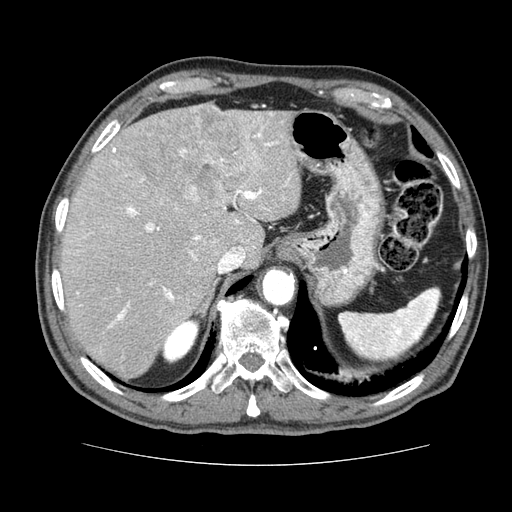
Contrast-enhanced abdominal CT (liver protocol), one axial slice; position 54 of 79 along the scan axis; soft-tissue window (W 400 / L 40 HU); 512 × 512 image matrix, field of view 360 × 360 mm. Case-level facts recorded for this patient, not image findings: diagnosis: hepatocellular carcinoma (patient treated with transarterial chemoembolisation; whether this scan precedes or follows treatment is not stated here); TNM stage (as recorded): Stage-I; Child-Pugh class: A; tumour nodularity: uninodular.
Outlined on this slice (semi-automatically segmented with operator editing):
- liver parenchyma outside the tumour (the mass and vessels are separate outlines, so this box may not span the whole liver): bounding box [x1, y1, x2, y2] px = [60, 102, 300, 378]
- mass: [141, 103, 250, 202]
- liver vessels: [76, 112, 290, 328]